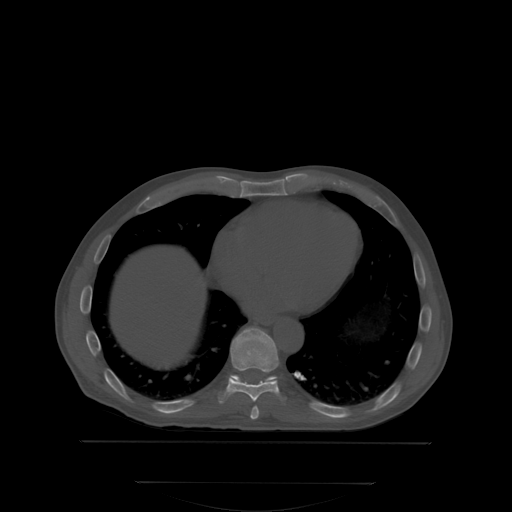
CT including the spine, one axial slice. Position 203 of 350 along the scan axis. Bone window (W 1800 / L 400 HU). 2.5 mm slice thickness. 512 × 512 image matrix. Patient: male, 58 years. From the clinical record (not read from this slice): primary cancer: prostate; vertebrae with lytic lesions (as recorded): L1.
Structures marked on this image (semi-automatic segmentation, software-assisted and operator-edited):
- T10 vertebra: bounding box <231,375,276,380> (left, top, right, bottom; pixels)
- T8 vertebra: <251,405,259,418>
- T9 vertebra: <226,328,285,402>